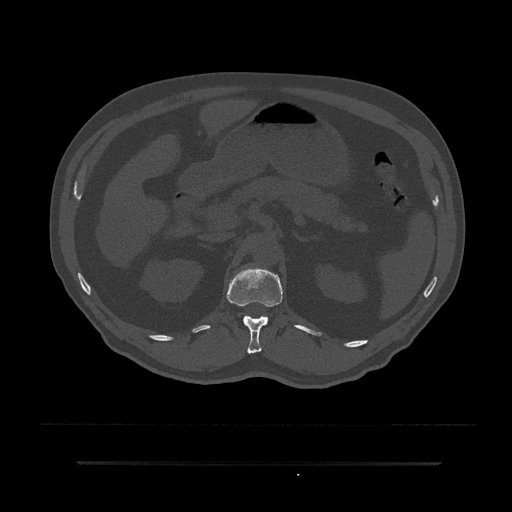
CT including the spine, one axial slice. Position 191 of 797 along the scan axis. 120 kVp. Bone window (W 1800 / L 400 HU). 0.5 mm slice thickness. 512 × 512 image matrix, field of view 464 × 464 mm. Patient: male, 59 years. From the clinical record (not read from this slice): primary cancer: bile ducts.
Annotated regions visible in this slice (semi-automatically segmented with operator editing):
- T12 vertebra: bounding box (x1, y1, x2, y2) in pixels: (227, 267, 283, 354)